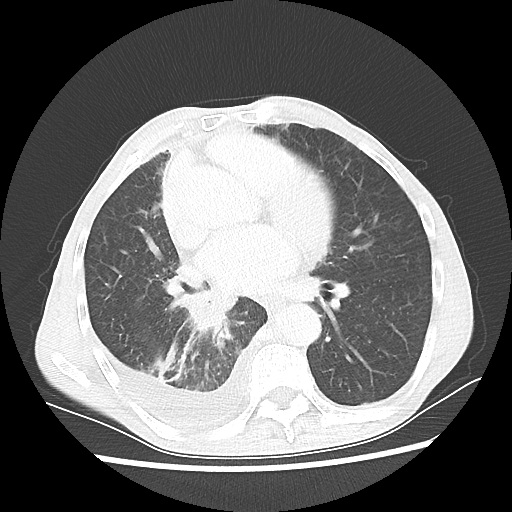
Chest CT, one axial slice; position 28 of 60 along the scan axis; lung window (W 1500 / L -600 HU); 512 × 512 image matrix, field of view 335 × 335 mm. Male patient, age 76 years. From the clinical record (not read from this slice): clinical TNM (as recorded): T3 N3 M1a; histopathological grade: G3.
Outlined on this slice (rectangle marked by the reading radiologist):
- lung tumour (recorded histology: squamous cell carcinoma): box from (x=176, y=290) to (x=234, y=351) px